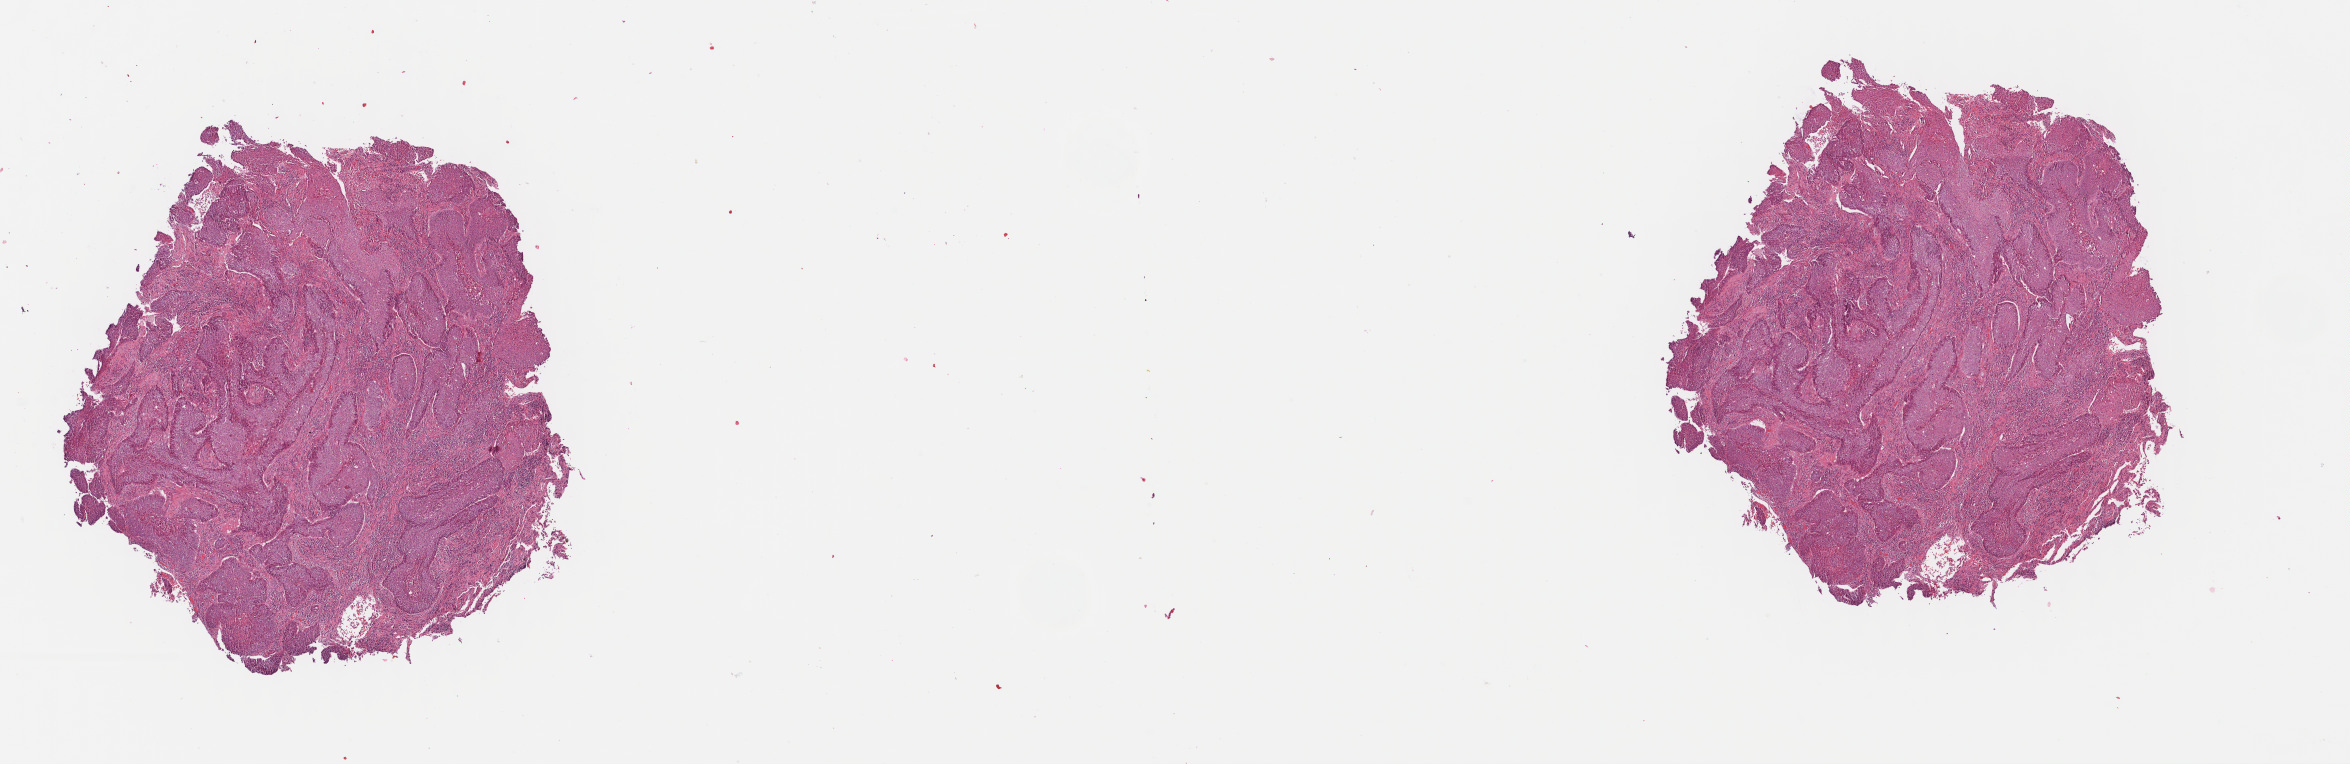
Digitized Hematoxylin and eosin (H&E) stained tissue section (whole slide), low-resolution overview of the scanned area, about 18.5 x 6.0 mm (from a 40x scan), formalin-fixed paraffin-embedded (FFPE) diagnostic section, sample: primary tumour, lung. Male, age 70 years at initial diagnosis.
Pathologic diagnosis: Squamous cell carcinoma, NOS (middle lobe, lung). AJCC pathologic stage: IB (7th edition).